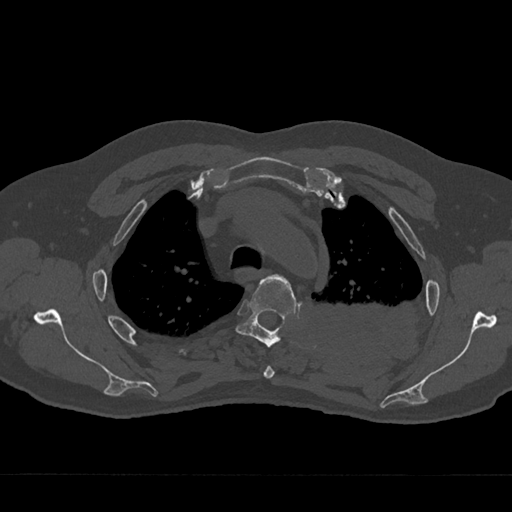
CT including the spine, one axial slice; slice 530 of 797 in the series (ordered by position); 120 kVp; bone window (W 1800 / L 400 HU); 512 × 512 image matrix, field of view 377 × 377 mm. Male patient, age 75 years. From the clinical record (not read from this slice): primary cancer: renal; vertebrae with lytic lesions (as recorded): T4.
Annotated regions visible in this slice (semi-automatically segmented with operator editing):
- T3 vertebra: box from (x=263, y=366) to (x=275, y=379) px
- T4 vertebra: (x=235, y=274)–(x=297, y=347)